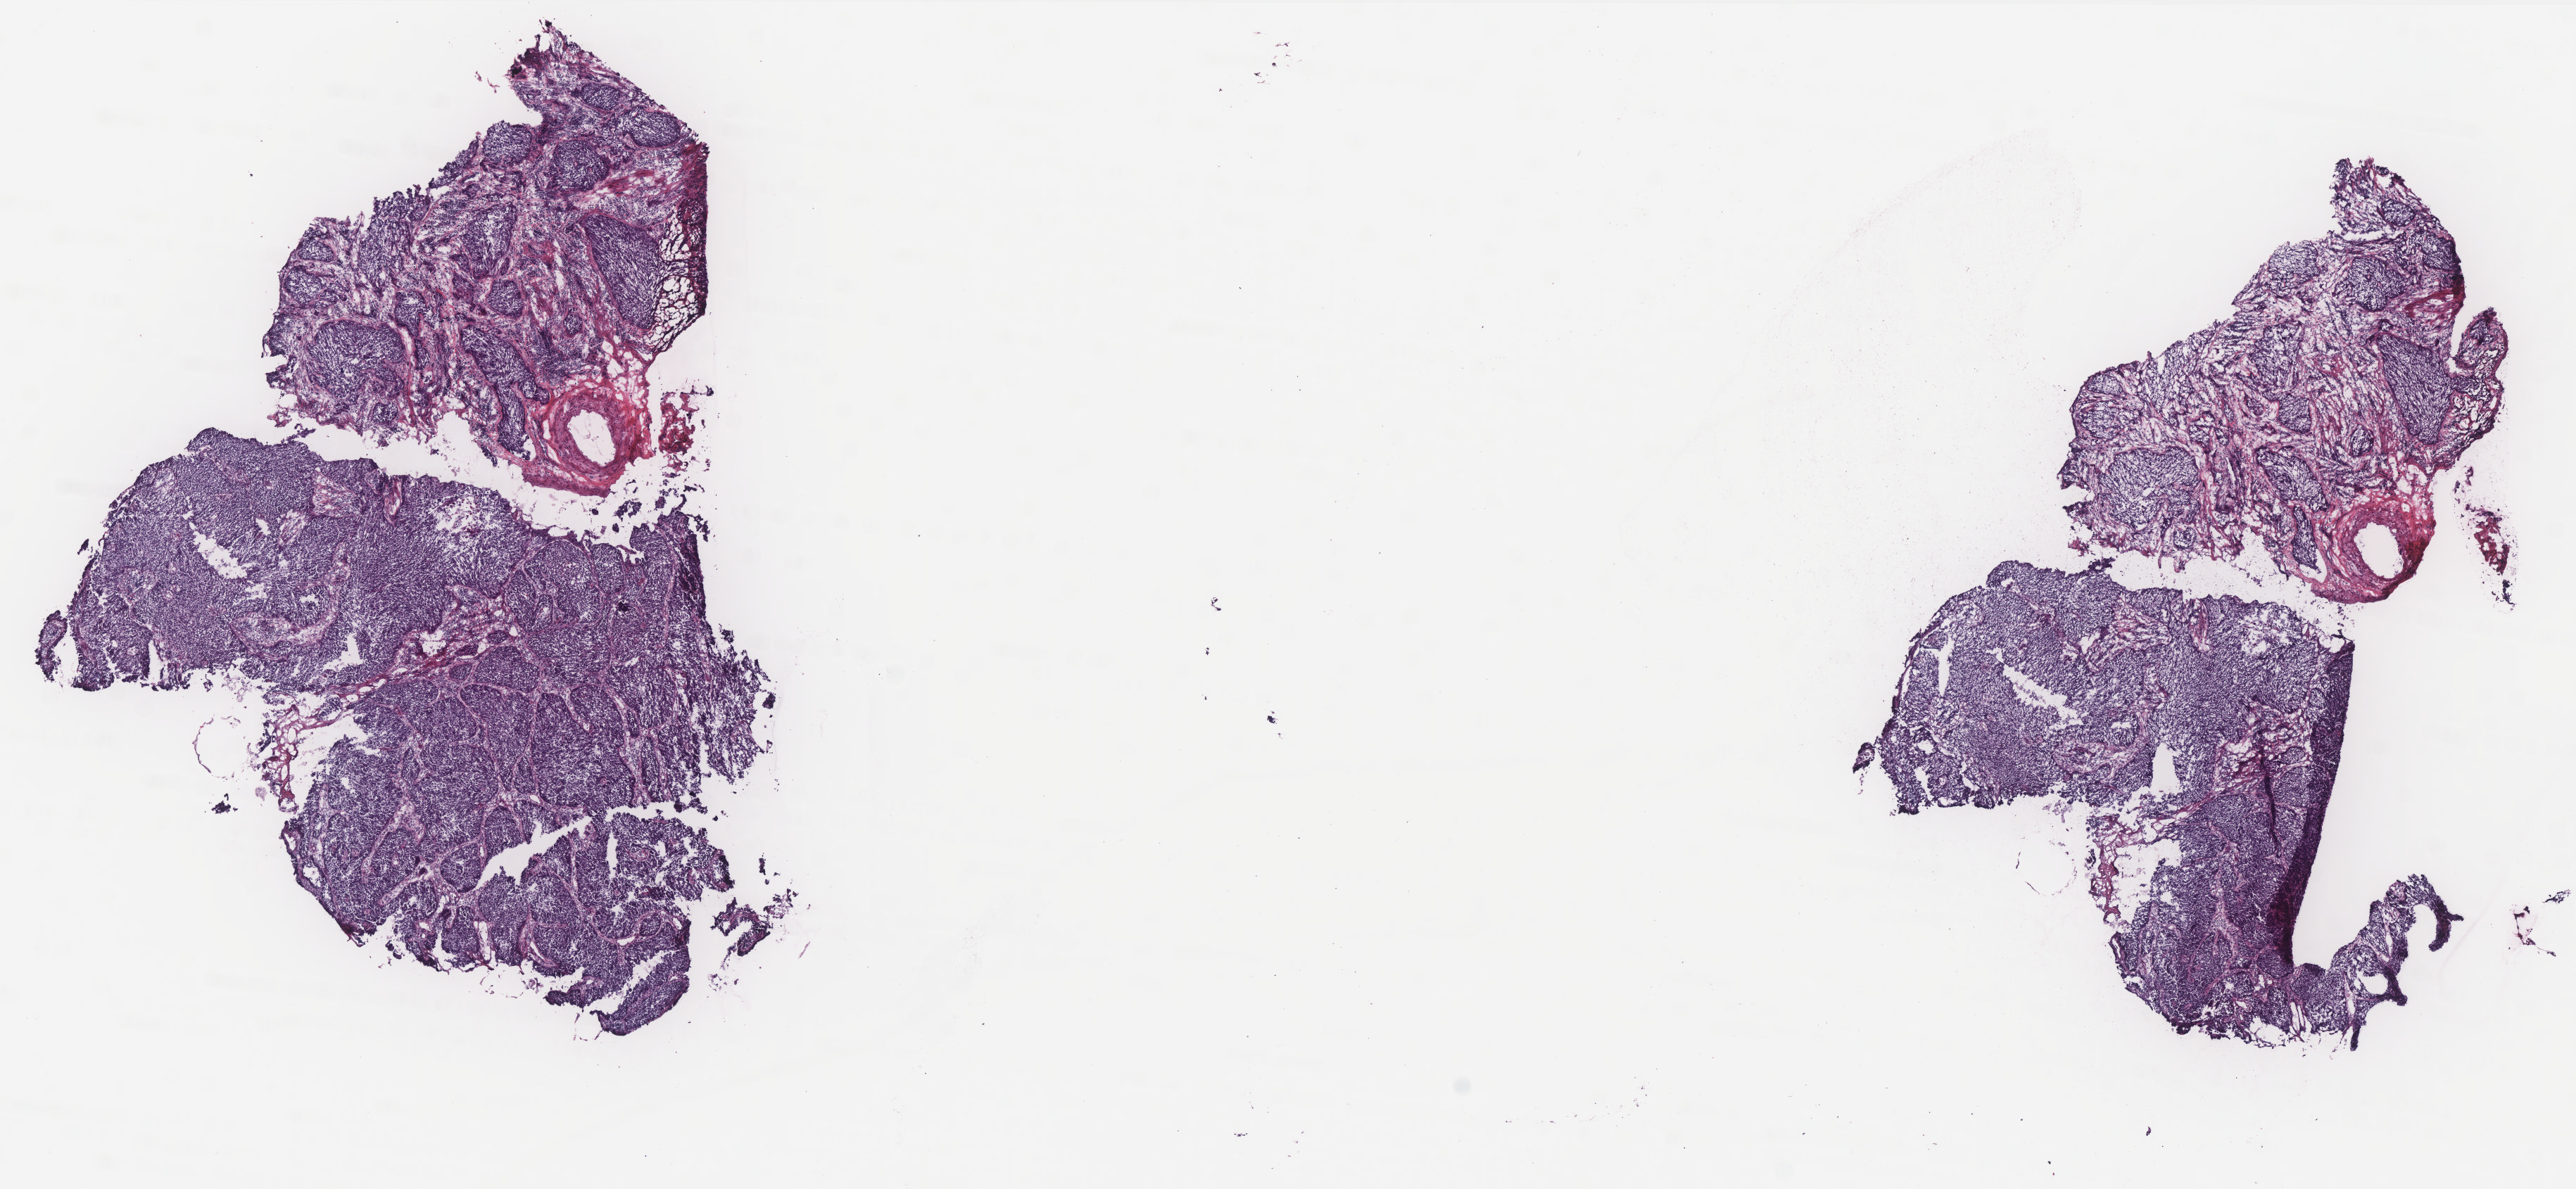
Whole-slide histology image, H&E — whole scanned area (about 14.7 x 6.8 mm, acquisition: 40x scan) shown as a low-resolution overview; frozen section; primary tumour sample from the cervix. Patient: female, age at initial diagnosis 25 years. Histologic grade: G2 (moderately differentiated). Pathologist review of this section (percent, as recorded): tumour cells 100%, tumour nuclei 75%, normal cells 0%, stromal cells 0%, necrosis 0%. Infiltration values recorded for this section: lymphocyte infiltration 0%, monocyte infiltration 0%, neutrophil infiltration 0%.
* histologic diagnosis: Squamous cell carcinoma, NOS (cervix uteri)
* lymph nodes positive (case pathology): 0 of 8 examined